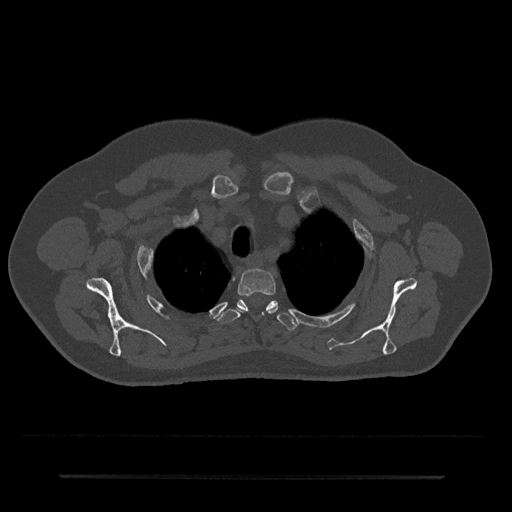
CT including the spine, one axial slice. Position 586 of 797 along the scan axis. Reconstruction kernel Br40s/3. 120 kVp. Bone window (W 1800 / L 400 HU). 0.5 mm slice thickness. 512 × 512 image matrix. Patient: male, 69 years. Case-level facts recorded for this patient, not image findings: primary cancer: prostate.
Annotated regions visible in this slice (semi-automatic segmentation, software-assisted and operator-edited):
- T2 vertebra: box from (x=237, y=268) to (x=277, y=313) px
- T3 vertebra: (x=217, y=299)–(x=298, y=330)